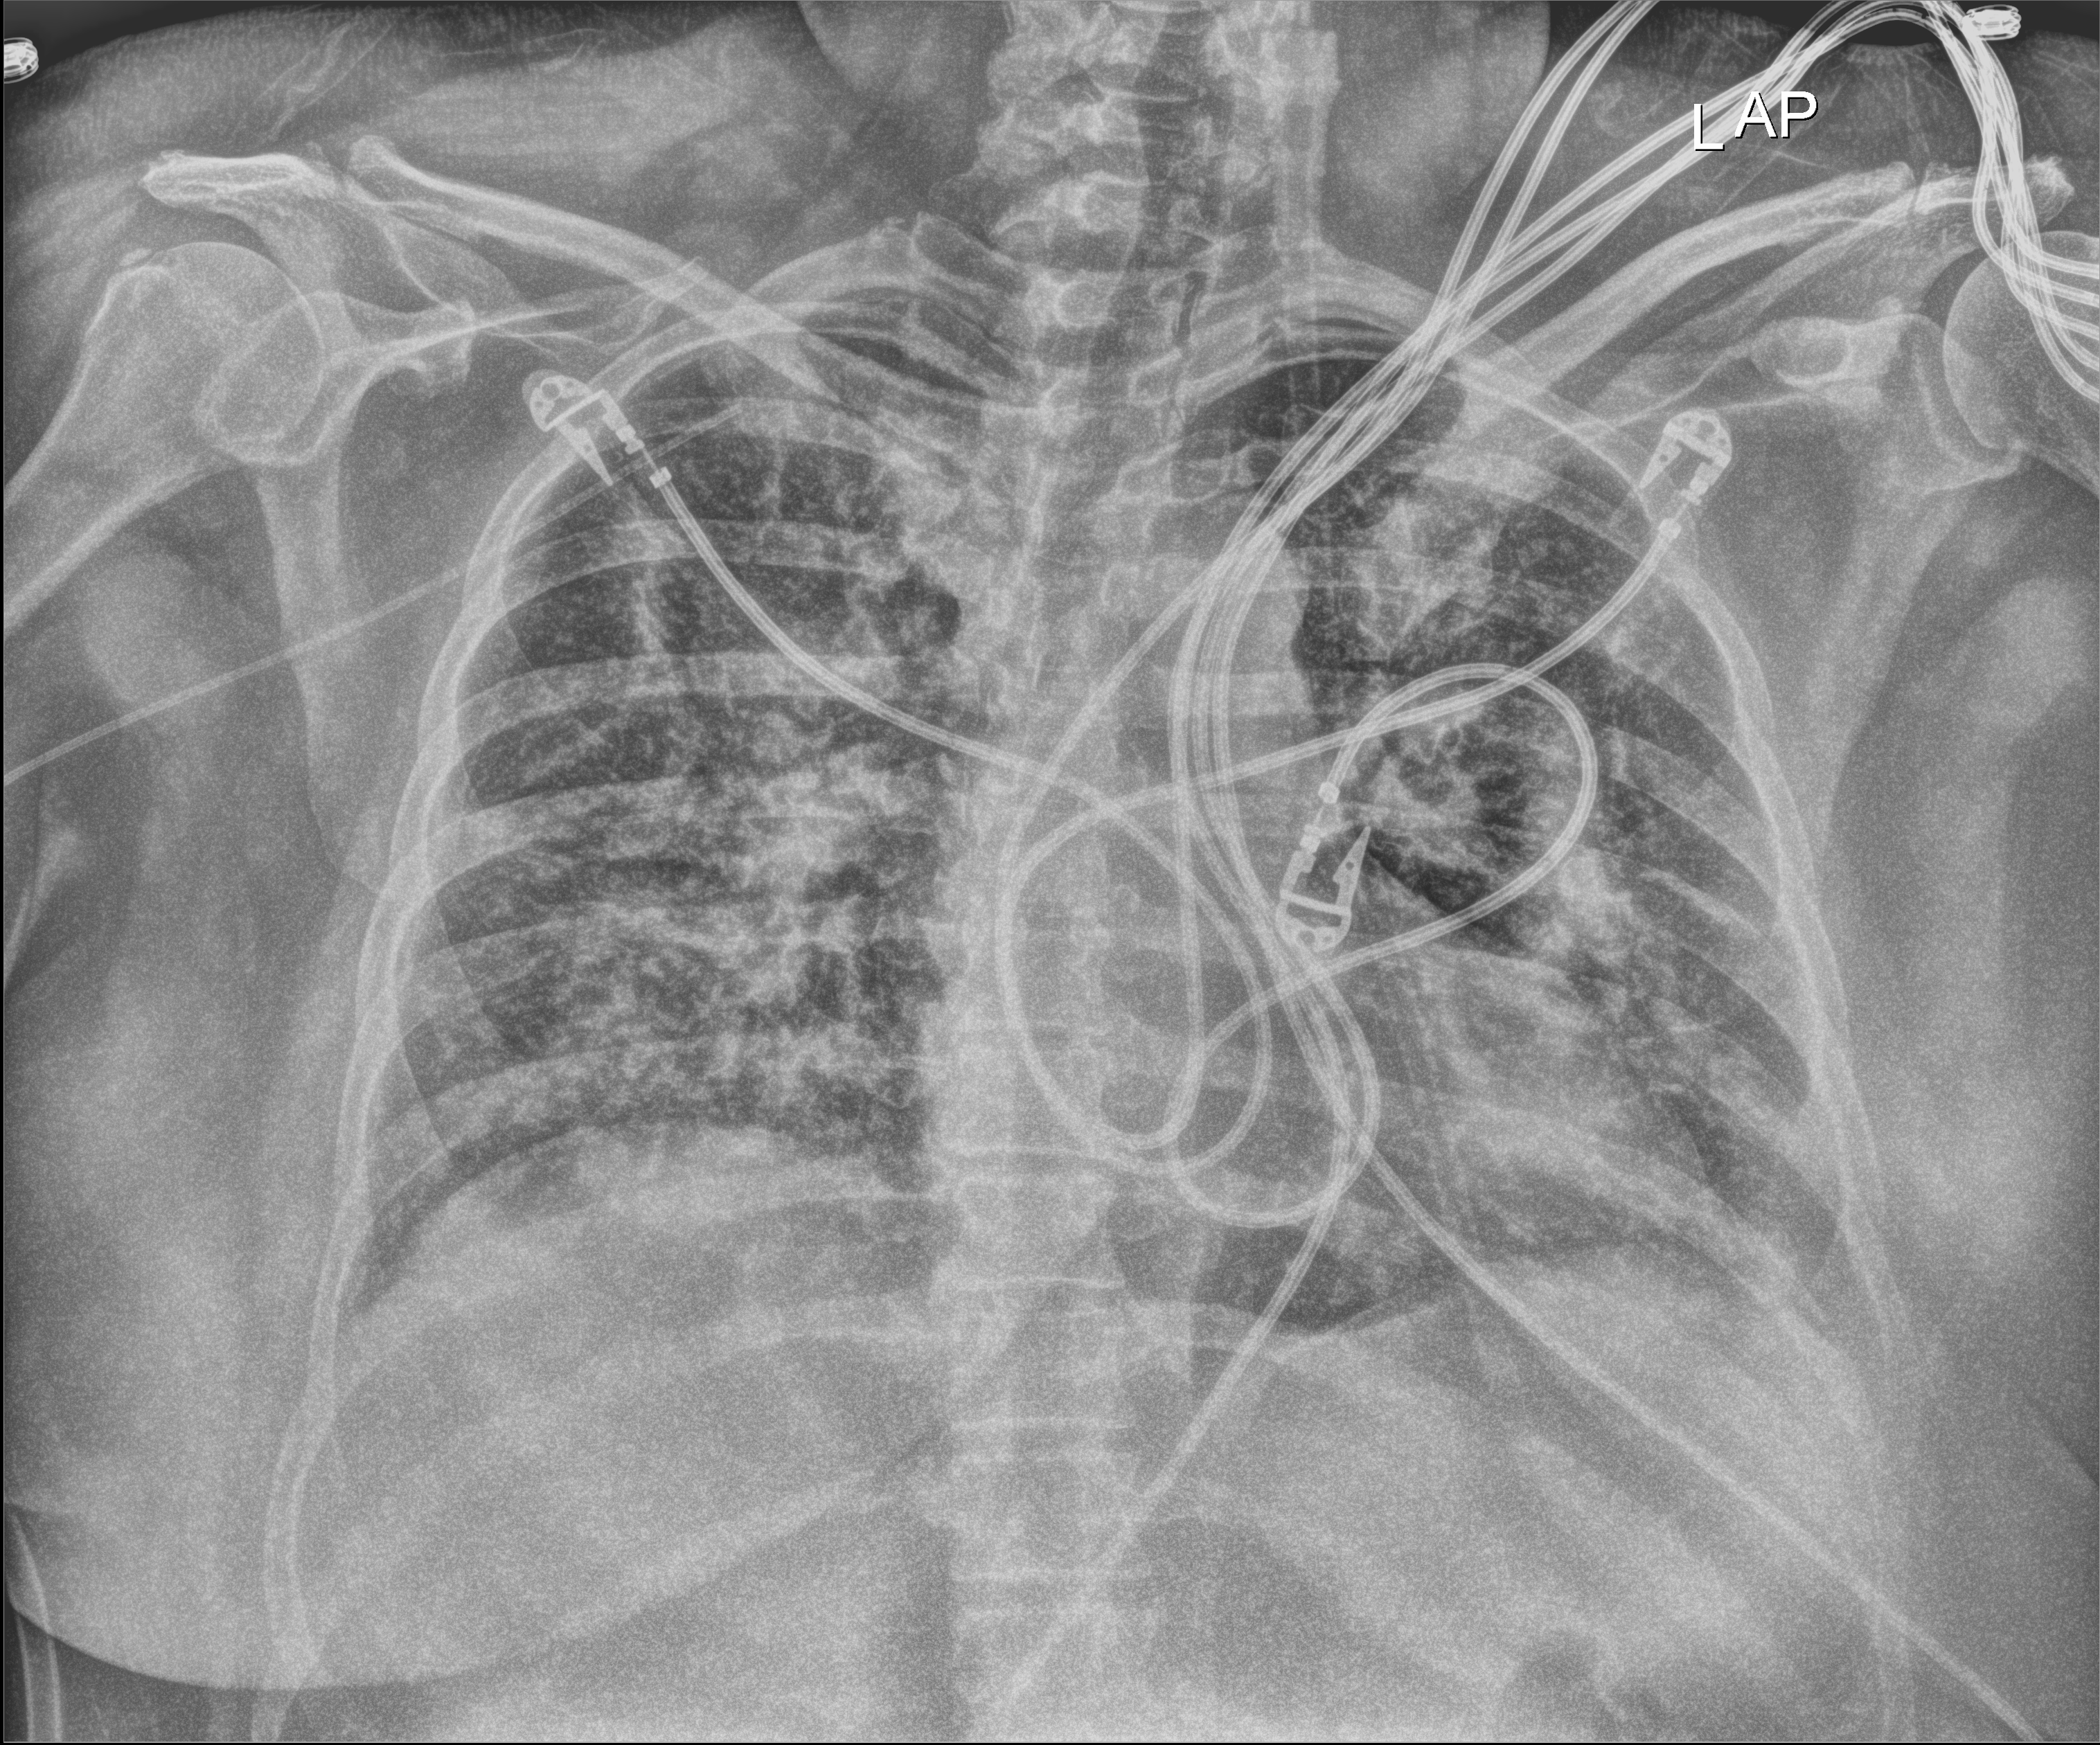
Chest X-ray (portable); anteroposterior (AP) projection. Patient hospitalised with COVID-19; female, aged 18–59 years.
Hospital-stay facts (about this admission, not read from this image; timing relative to this image not recorded): chronic kidney disease (admission record): no; admitted to intensive care during this hospital stay: no.